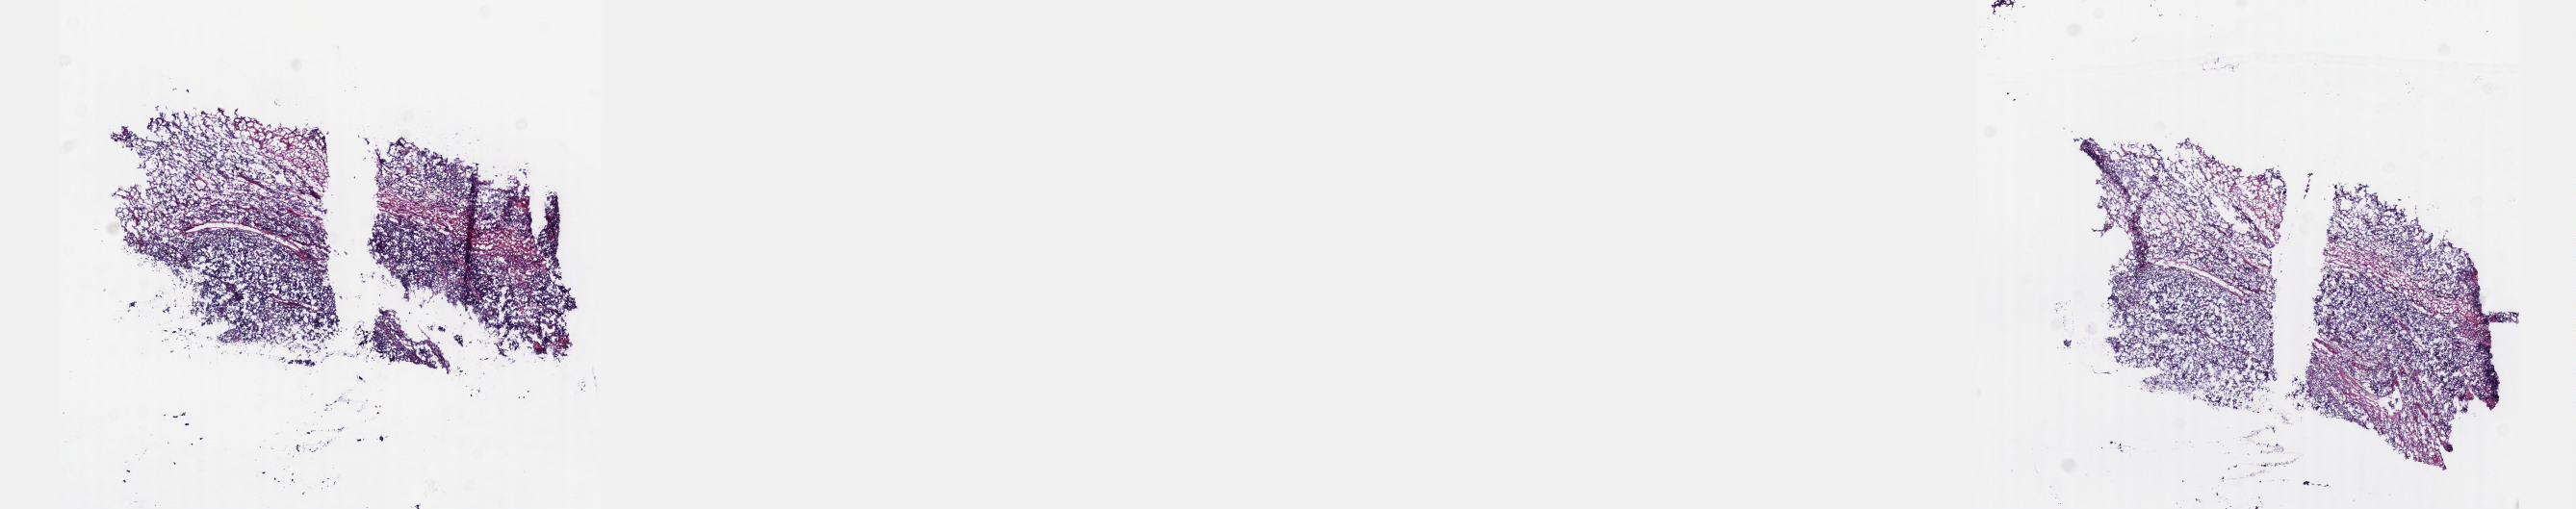
Digitized H&E tissue section (whole slide), a low-resolution overview of the entire scanned area, about 21.6 x 4.3 mm (slide scanned at 40x); frozen section; primary tumour sample from the testis. Male patient; age at initial diagnosis 25 years. Composition of this section per pathologist review: tumour cells 80%, tumour nuclei 80%, normal cells 0%, stromal cells 10%, necrosis 10%. Infiltration values recorded for this section: lymphocyte infiltration 40%, monocyte infiltration 20%, neutrophil infiltration 20%.
Pathologic diagnosis: Embryonal carcinoma, NOS. Laterality: left. AJCC pathologic stage: IA (6th edition).